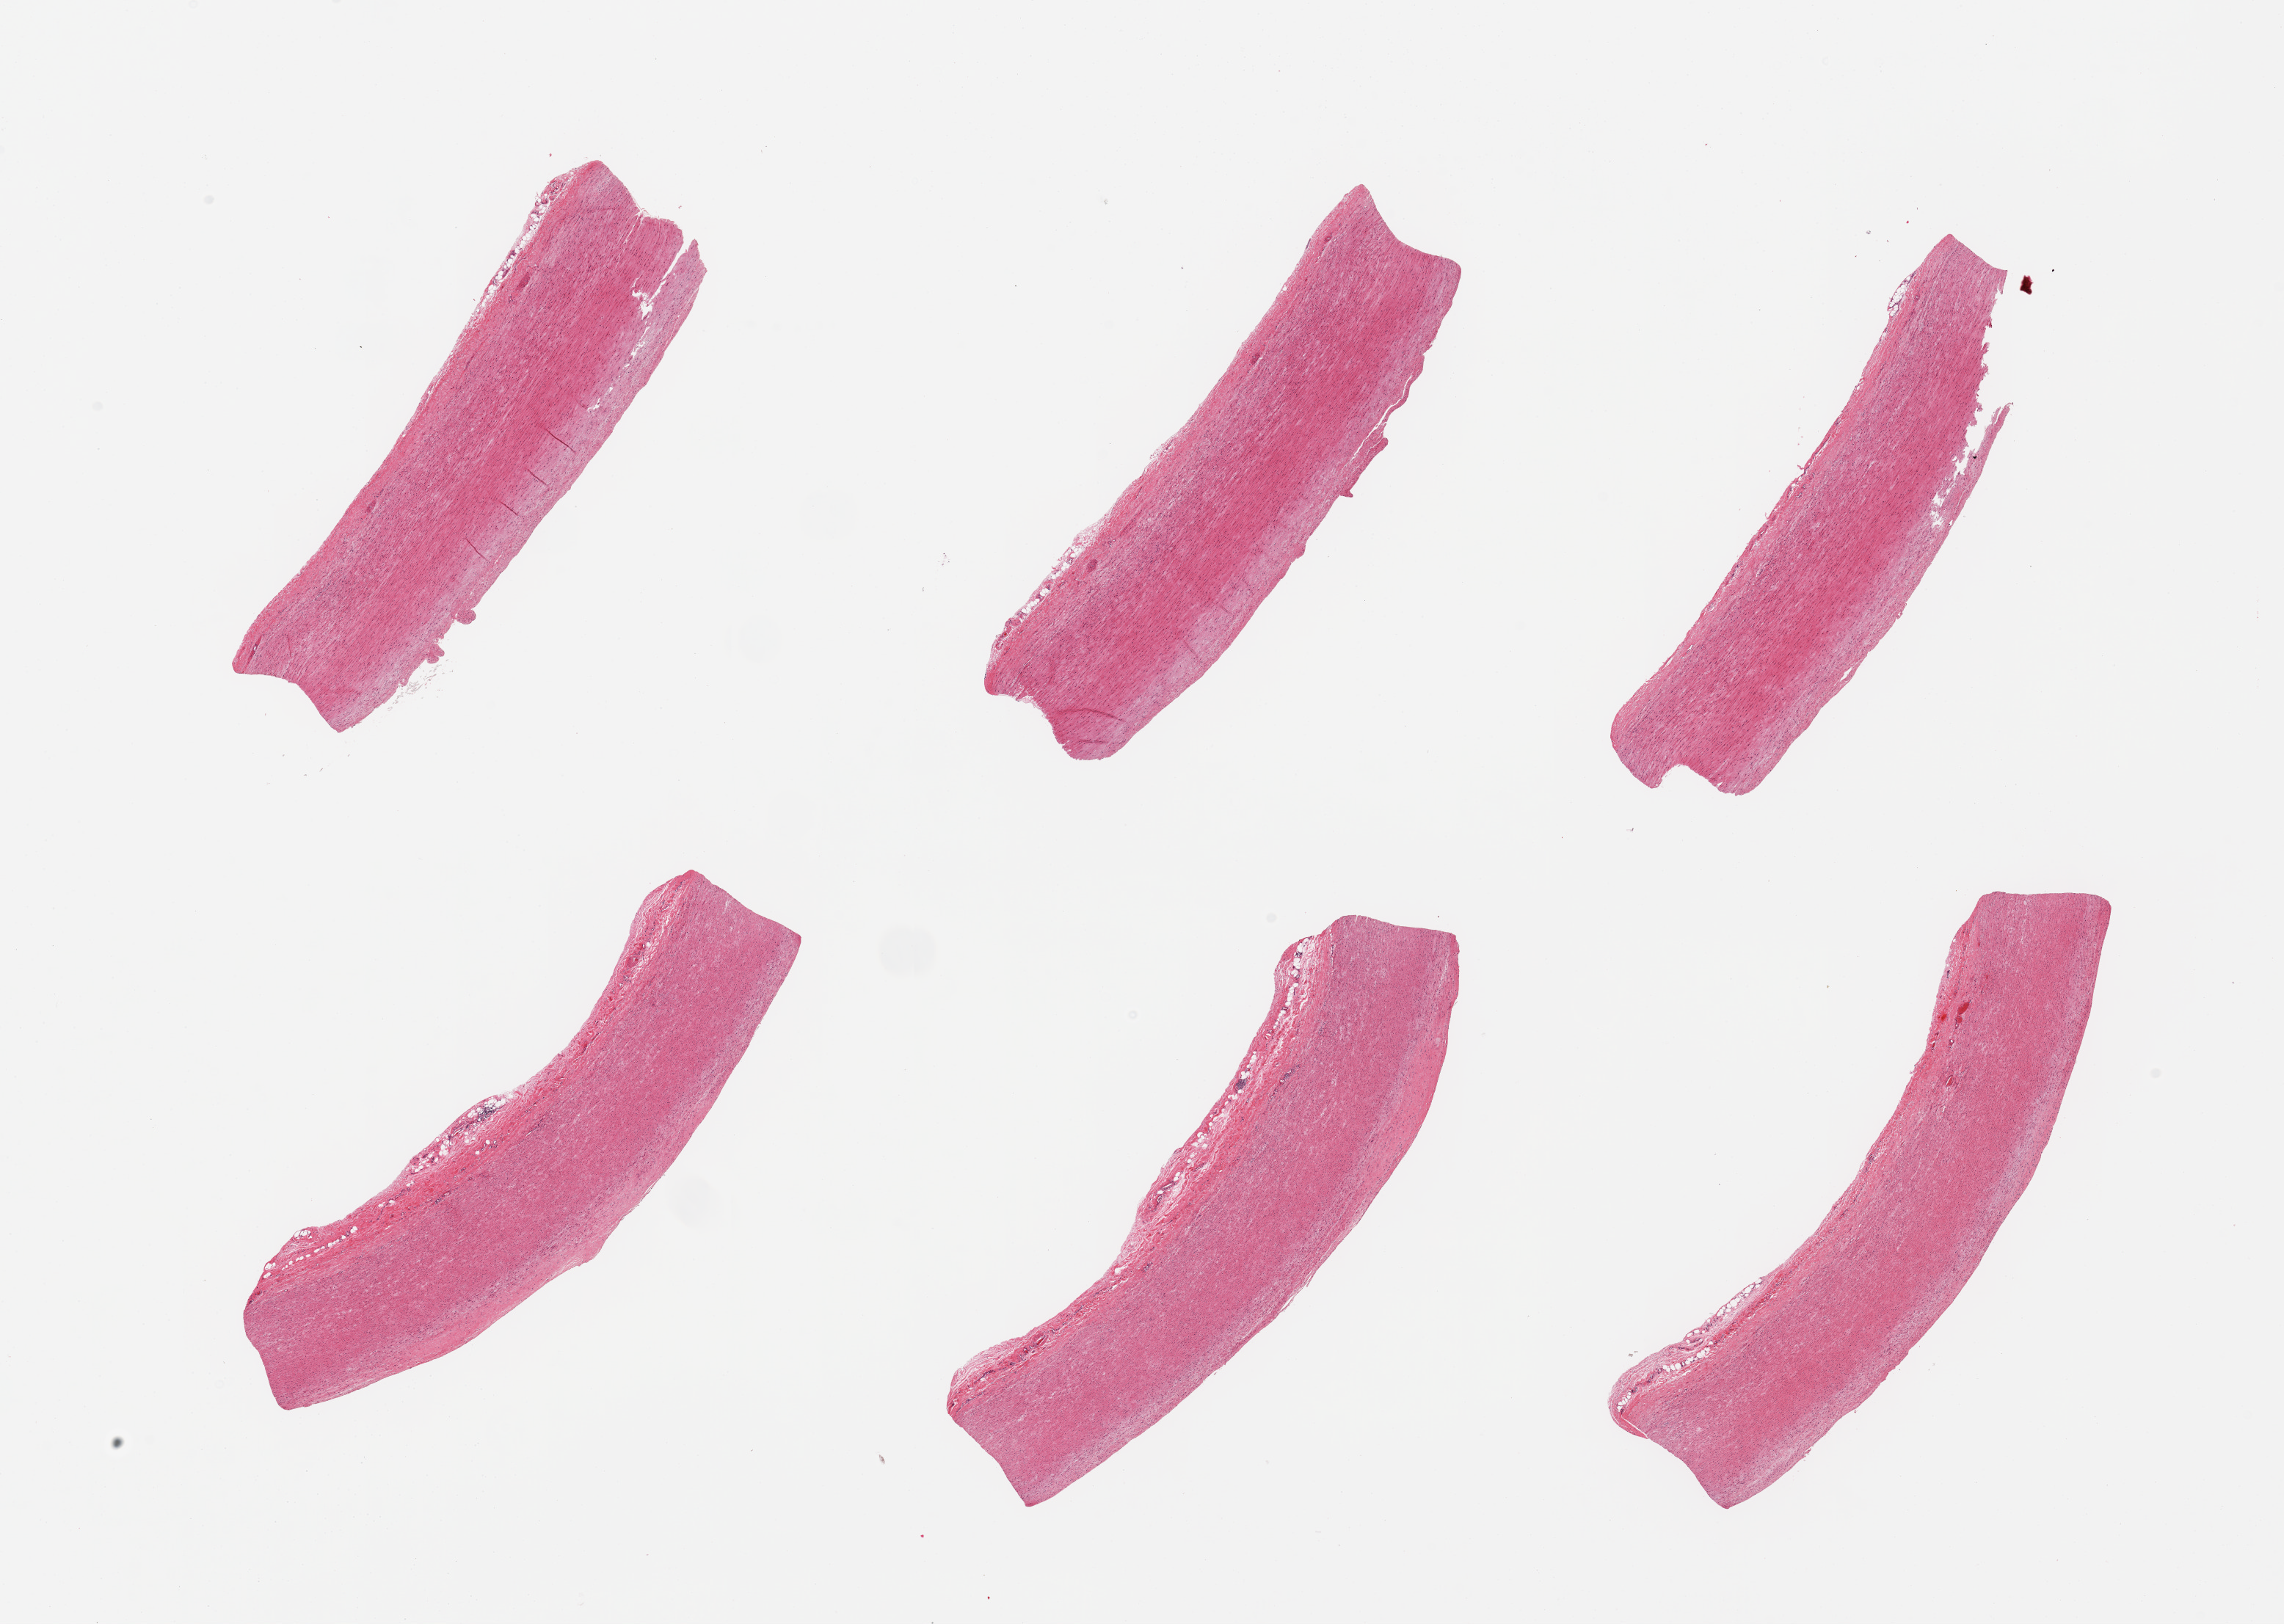
Whole-slide image, H&E stain — whole scanned area (about 24.6 x 17.5 mm, from a 20x scan) shown as a low-resolution overview; PAXgene-fixed paraffin-embedded (PFPE) section; sampled site (target tissue): aorta; donor tissue sample. Male donor.
- pathologist's review note for this sample: 6 pieces; atherosclerosis